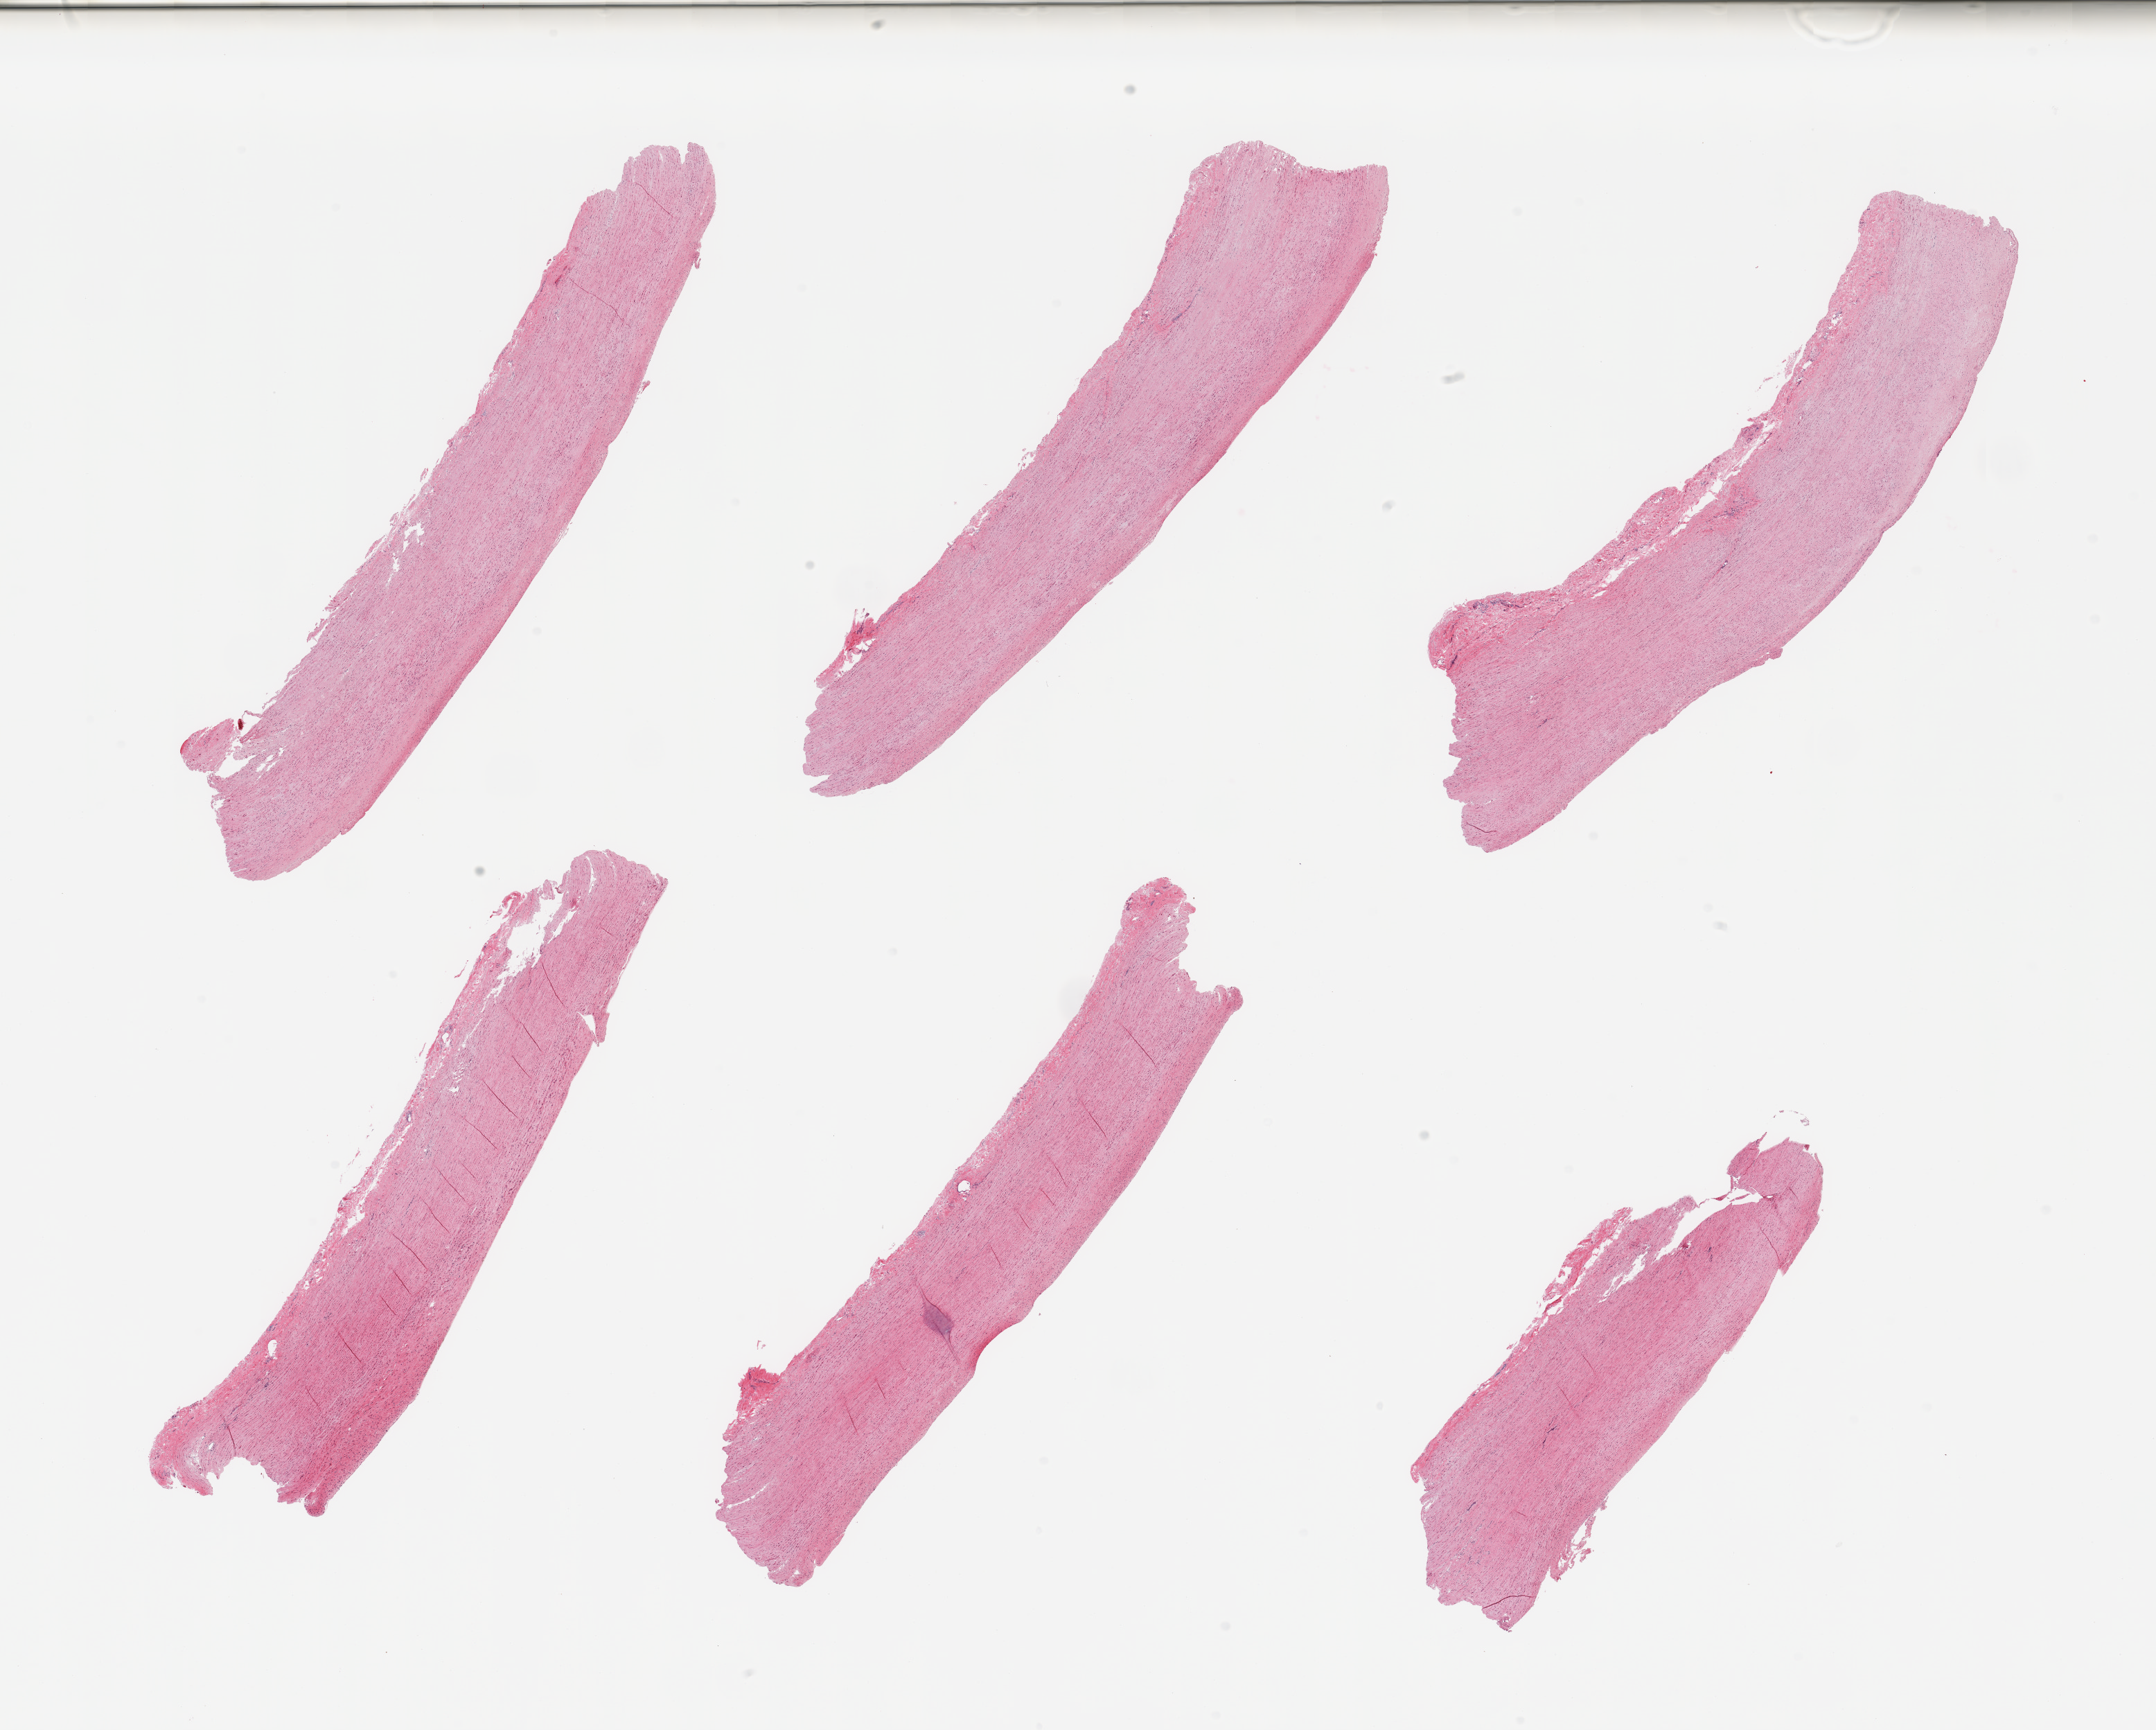
Whole-slide image, hematoxylin and eosin (H&E) stain — whole scanned area (about 24.6 x 19.7 mm) shown as a low-resolution overview. PAXgene-fixed, paraffin-embedded tissue. Sampled site (target tissue): aorta. Tissue donor sample. Donor: male.
Reviewer comment on this tissue sample: 6 pieces; well trimmed; minimal plaque.